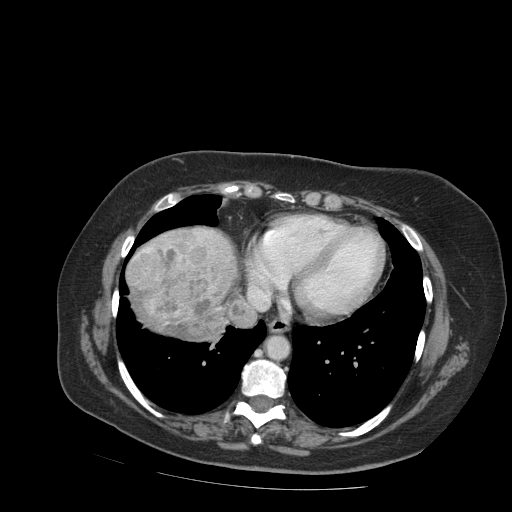
Contrast-enhanced abdominal CT (liver protocol), one axial slice. Position 85 of 99 along the scan axis. Reconstruction kernel STANDARD. 140 kVp. Soft-tissue window (W 400 / L 40 HU). 512 × 512 image matrix, field of view 400 × 400 mm. From the clinical record (not read from this slice): diagnosis: hepatocellular carcinoma (patient treated with transarterial chemoembolisation; whether this scan precedes or follows treatment is not stated here); TNM stage (as recorded): Stage-IVB; Child-Pugh class: A; tumour differentiation: moderately differentiated; tumour nodularity: uninodular.
Structures marked on this image (semi-automatic segmentation, software-assisted and operator-edited):
- liver parenchyma outside the tumour (the mass and vessels are separate outlines, so this box may not span the whole liver): bounding box [x1, y1, x2, y2] px = [126, 226, 251, 340]
- mass: [130, 245, 238, 339]
- liver vessels: [143, 248, 151, 251]